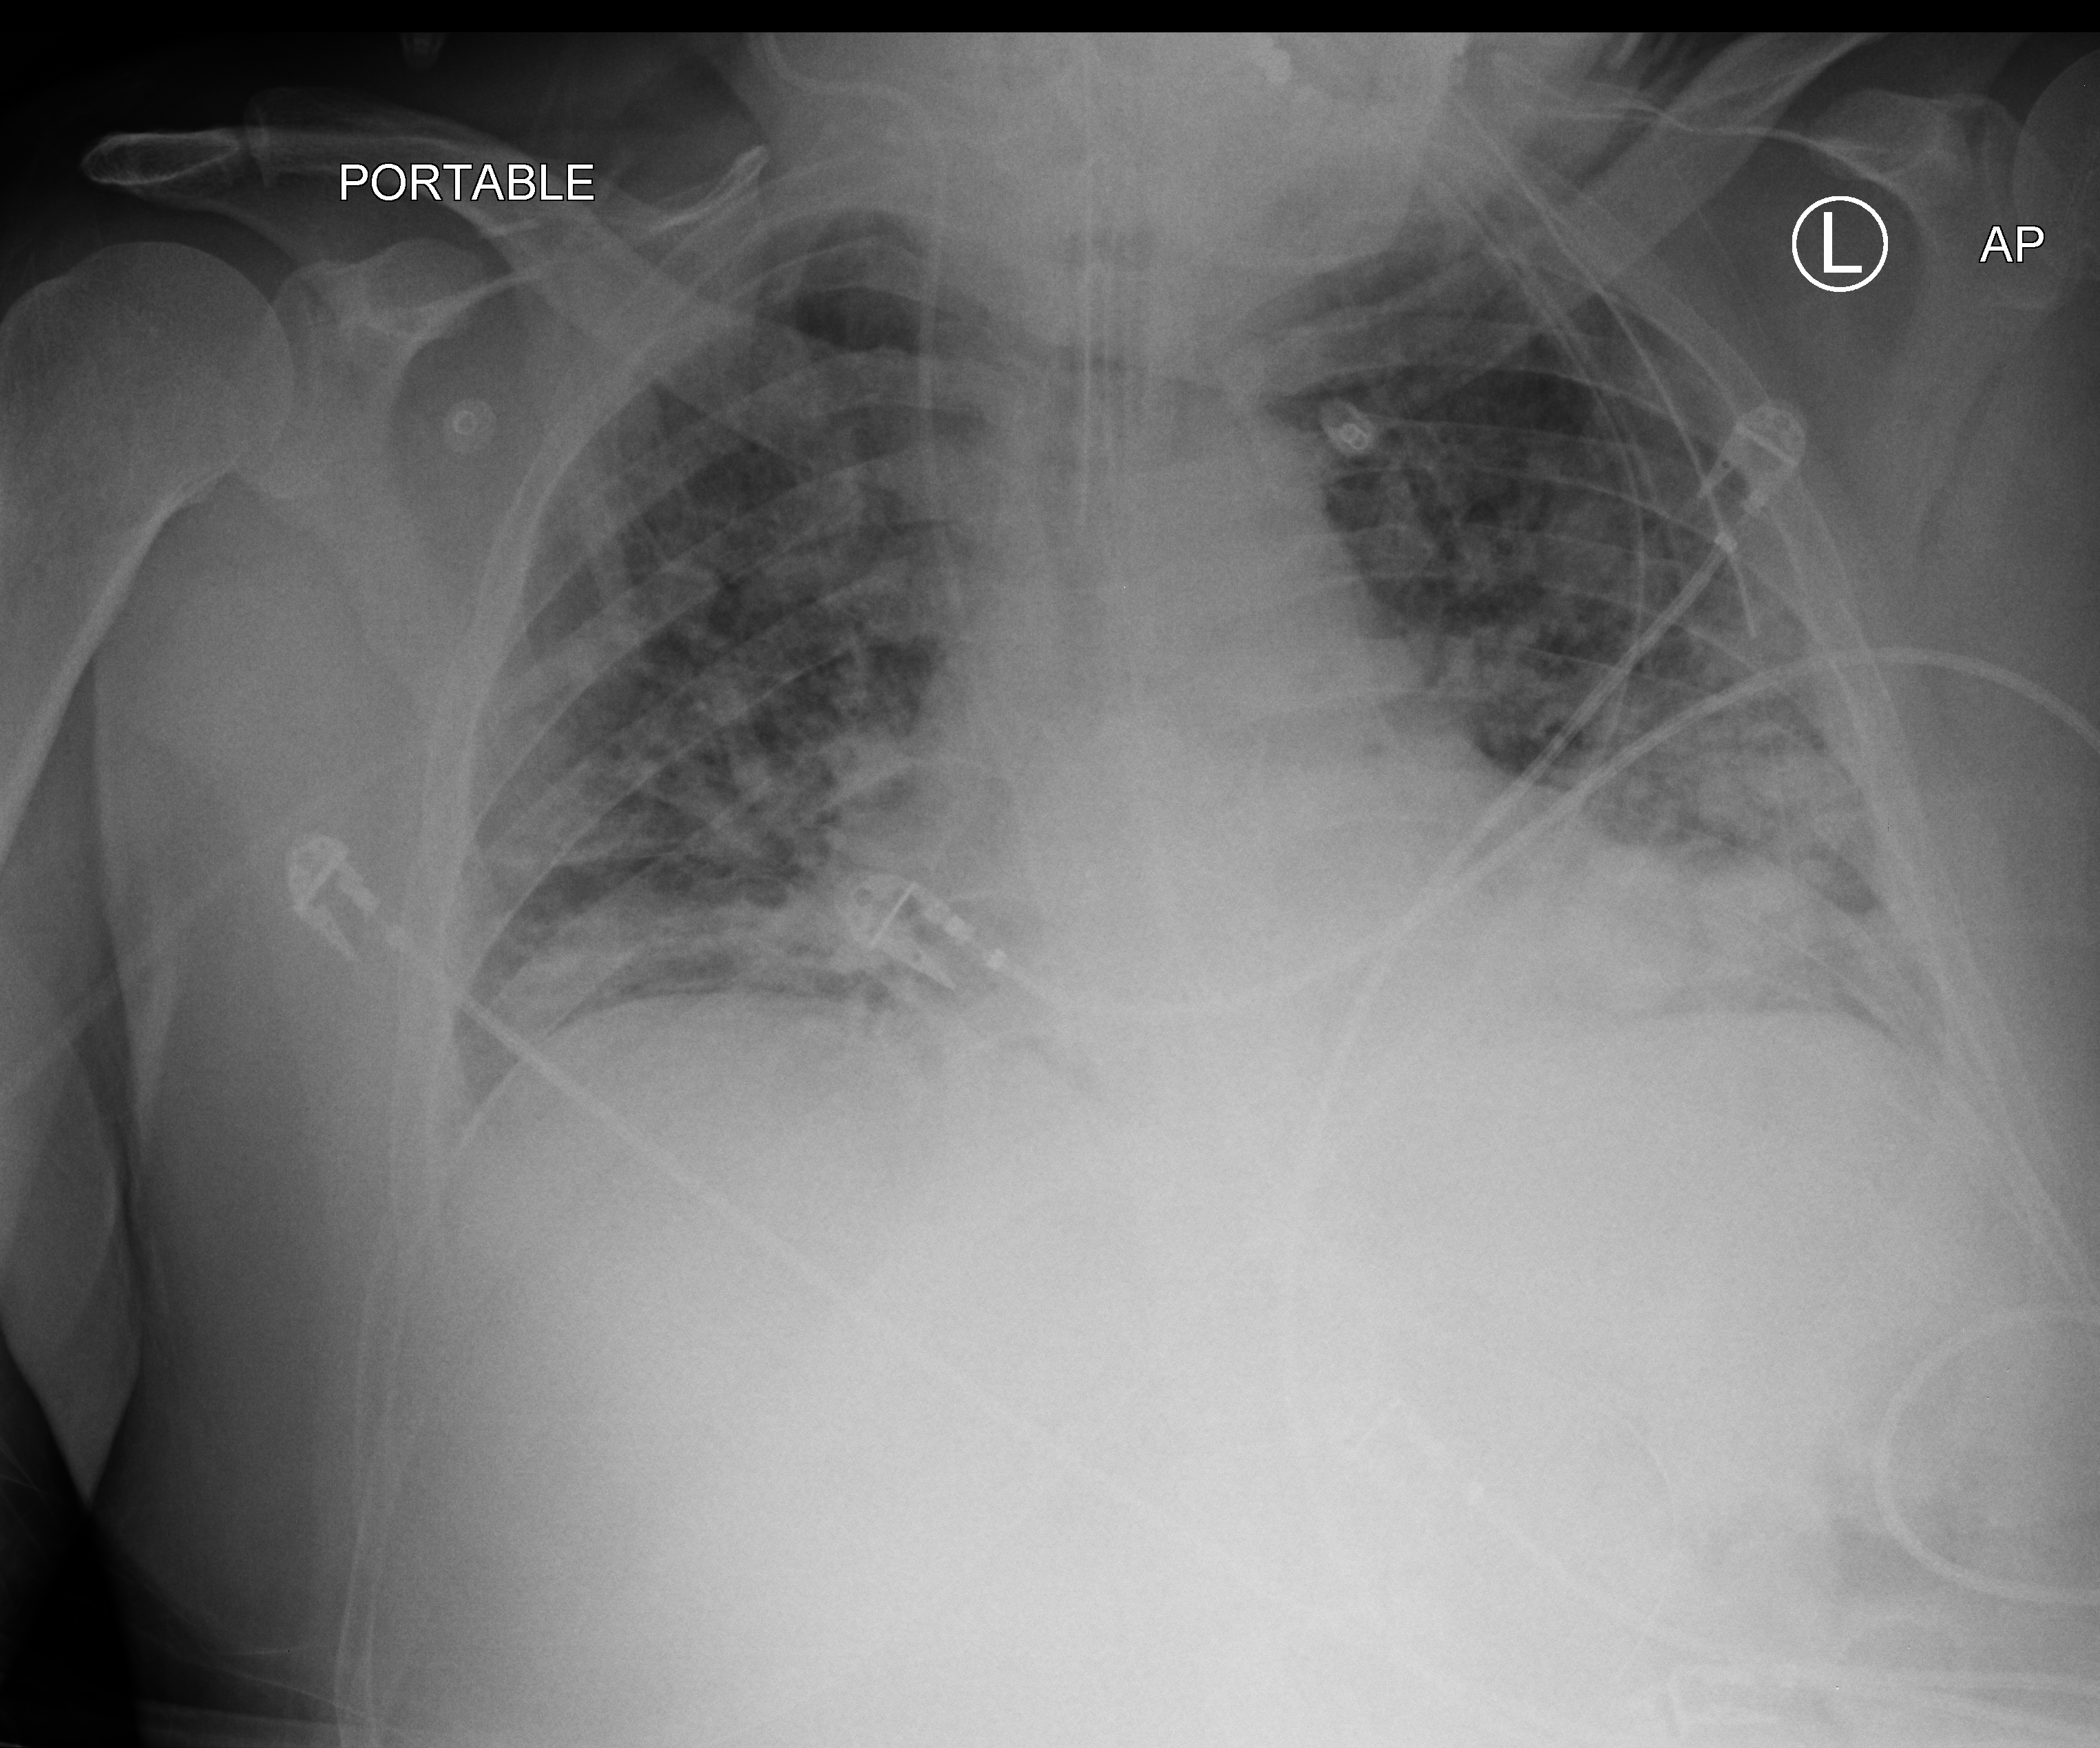
Chest X-ray (portable), anteroposterior (AP) projection. Patient hospitalised with COVID-19; male, aged 18–59 years.
Hospital-stay facts (about this admission, not read from this image; timing relative to this image not recorded): mechanically ventilated during this hospital stay: yes; admitted to intensive care during this hospital stay: yes.